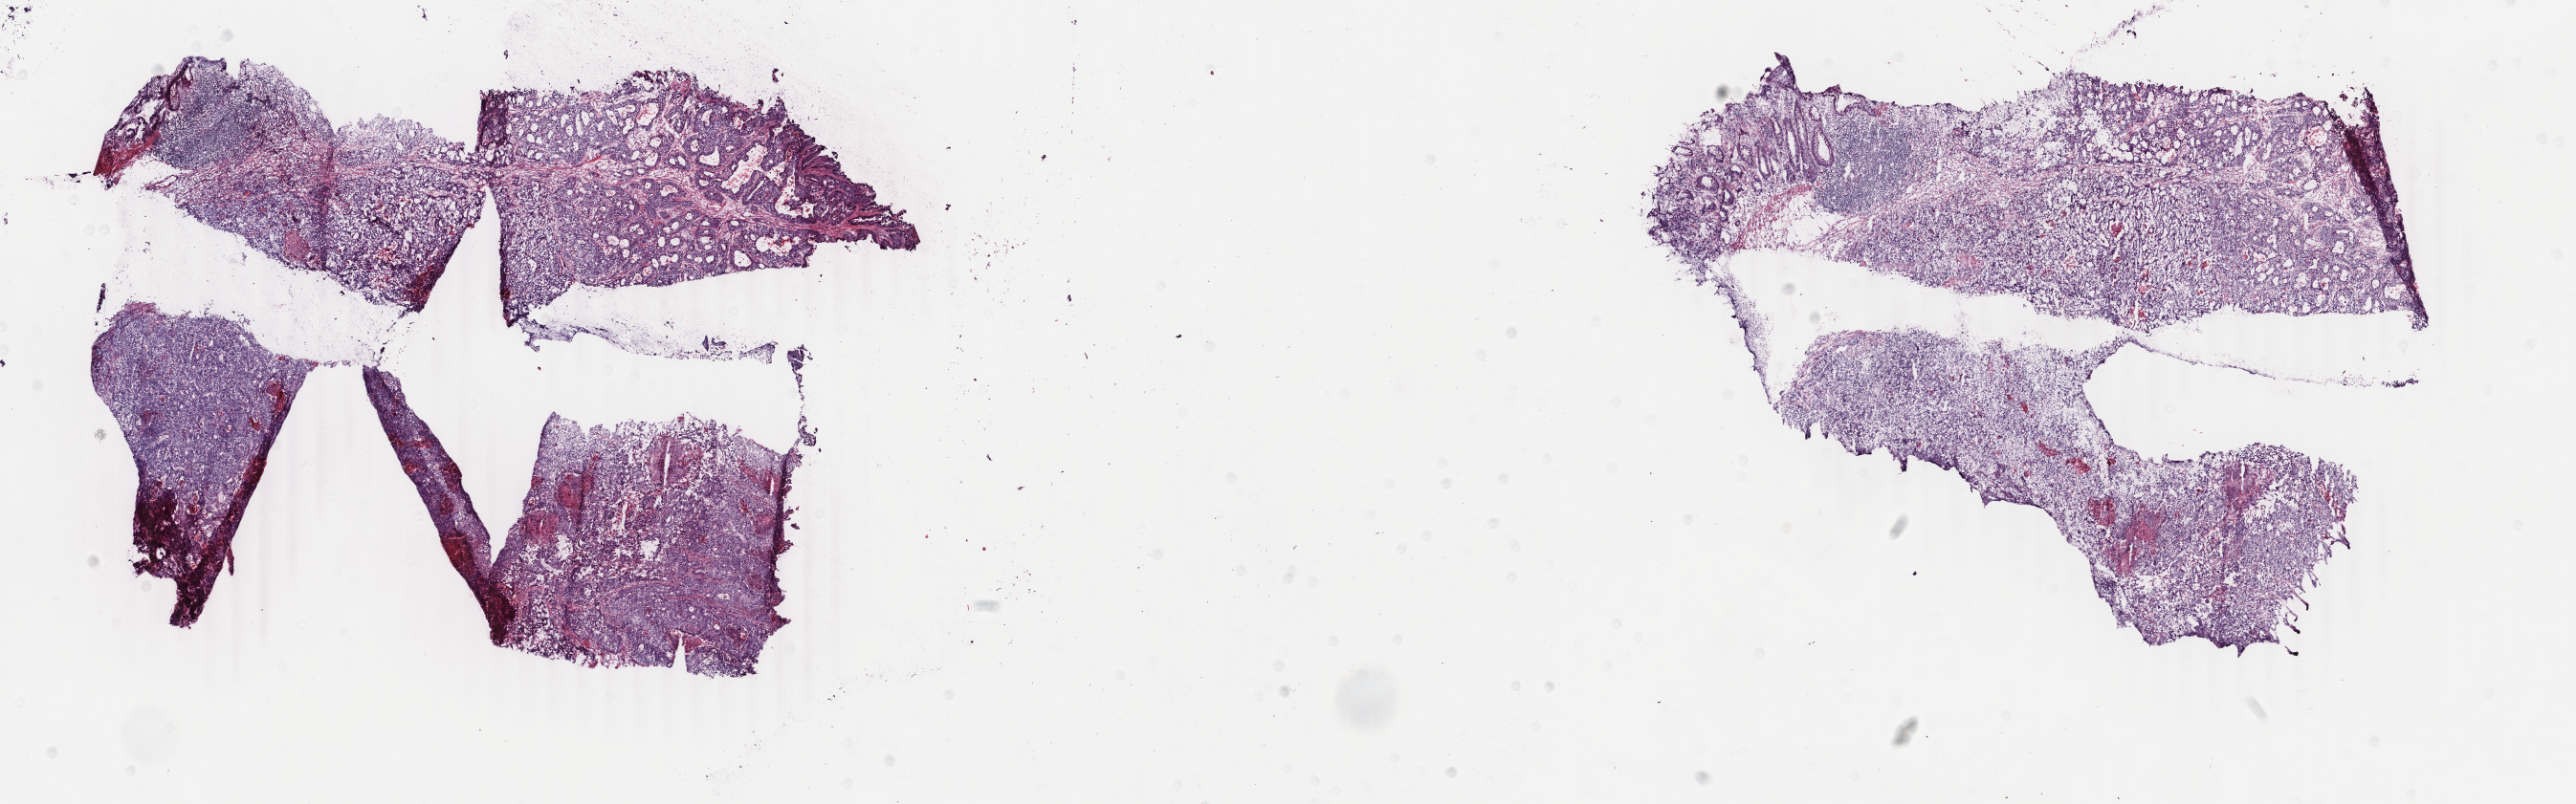
Digitized Hematoxylin and eosin (H&E) stained tissue section (whole slide) — low-resolution overview of the scanned area, about 21.4 x 6.7 mm (slide scanned at 40x). Frozen section. Colon, primary tumour sample. Male patient; age at initial diagnosis 50 years. Slide review estimates, as recorded: tumour cells 72%, tumour nuclei 70%, normal cells 8%, stromal cells 10%, necrosis 10%. Inflammatory infiltration, as recorded: lymphocyte infiltration 22%, monocyte infiltration 0%, neutrophil infiltration 2%.
AJCC pathologic stage: IV. Histologic diagnosis: Adenocarcinoma, NOS (ascending colon).